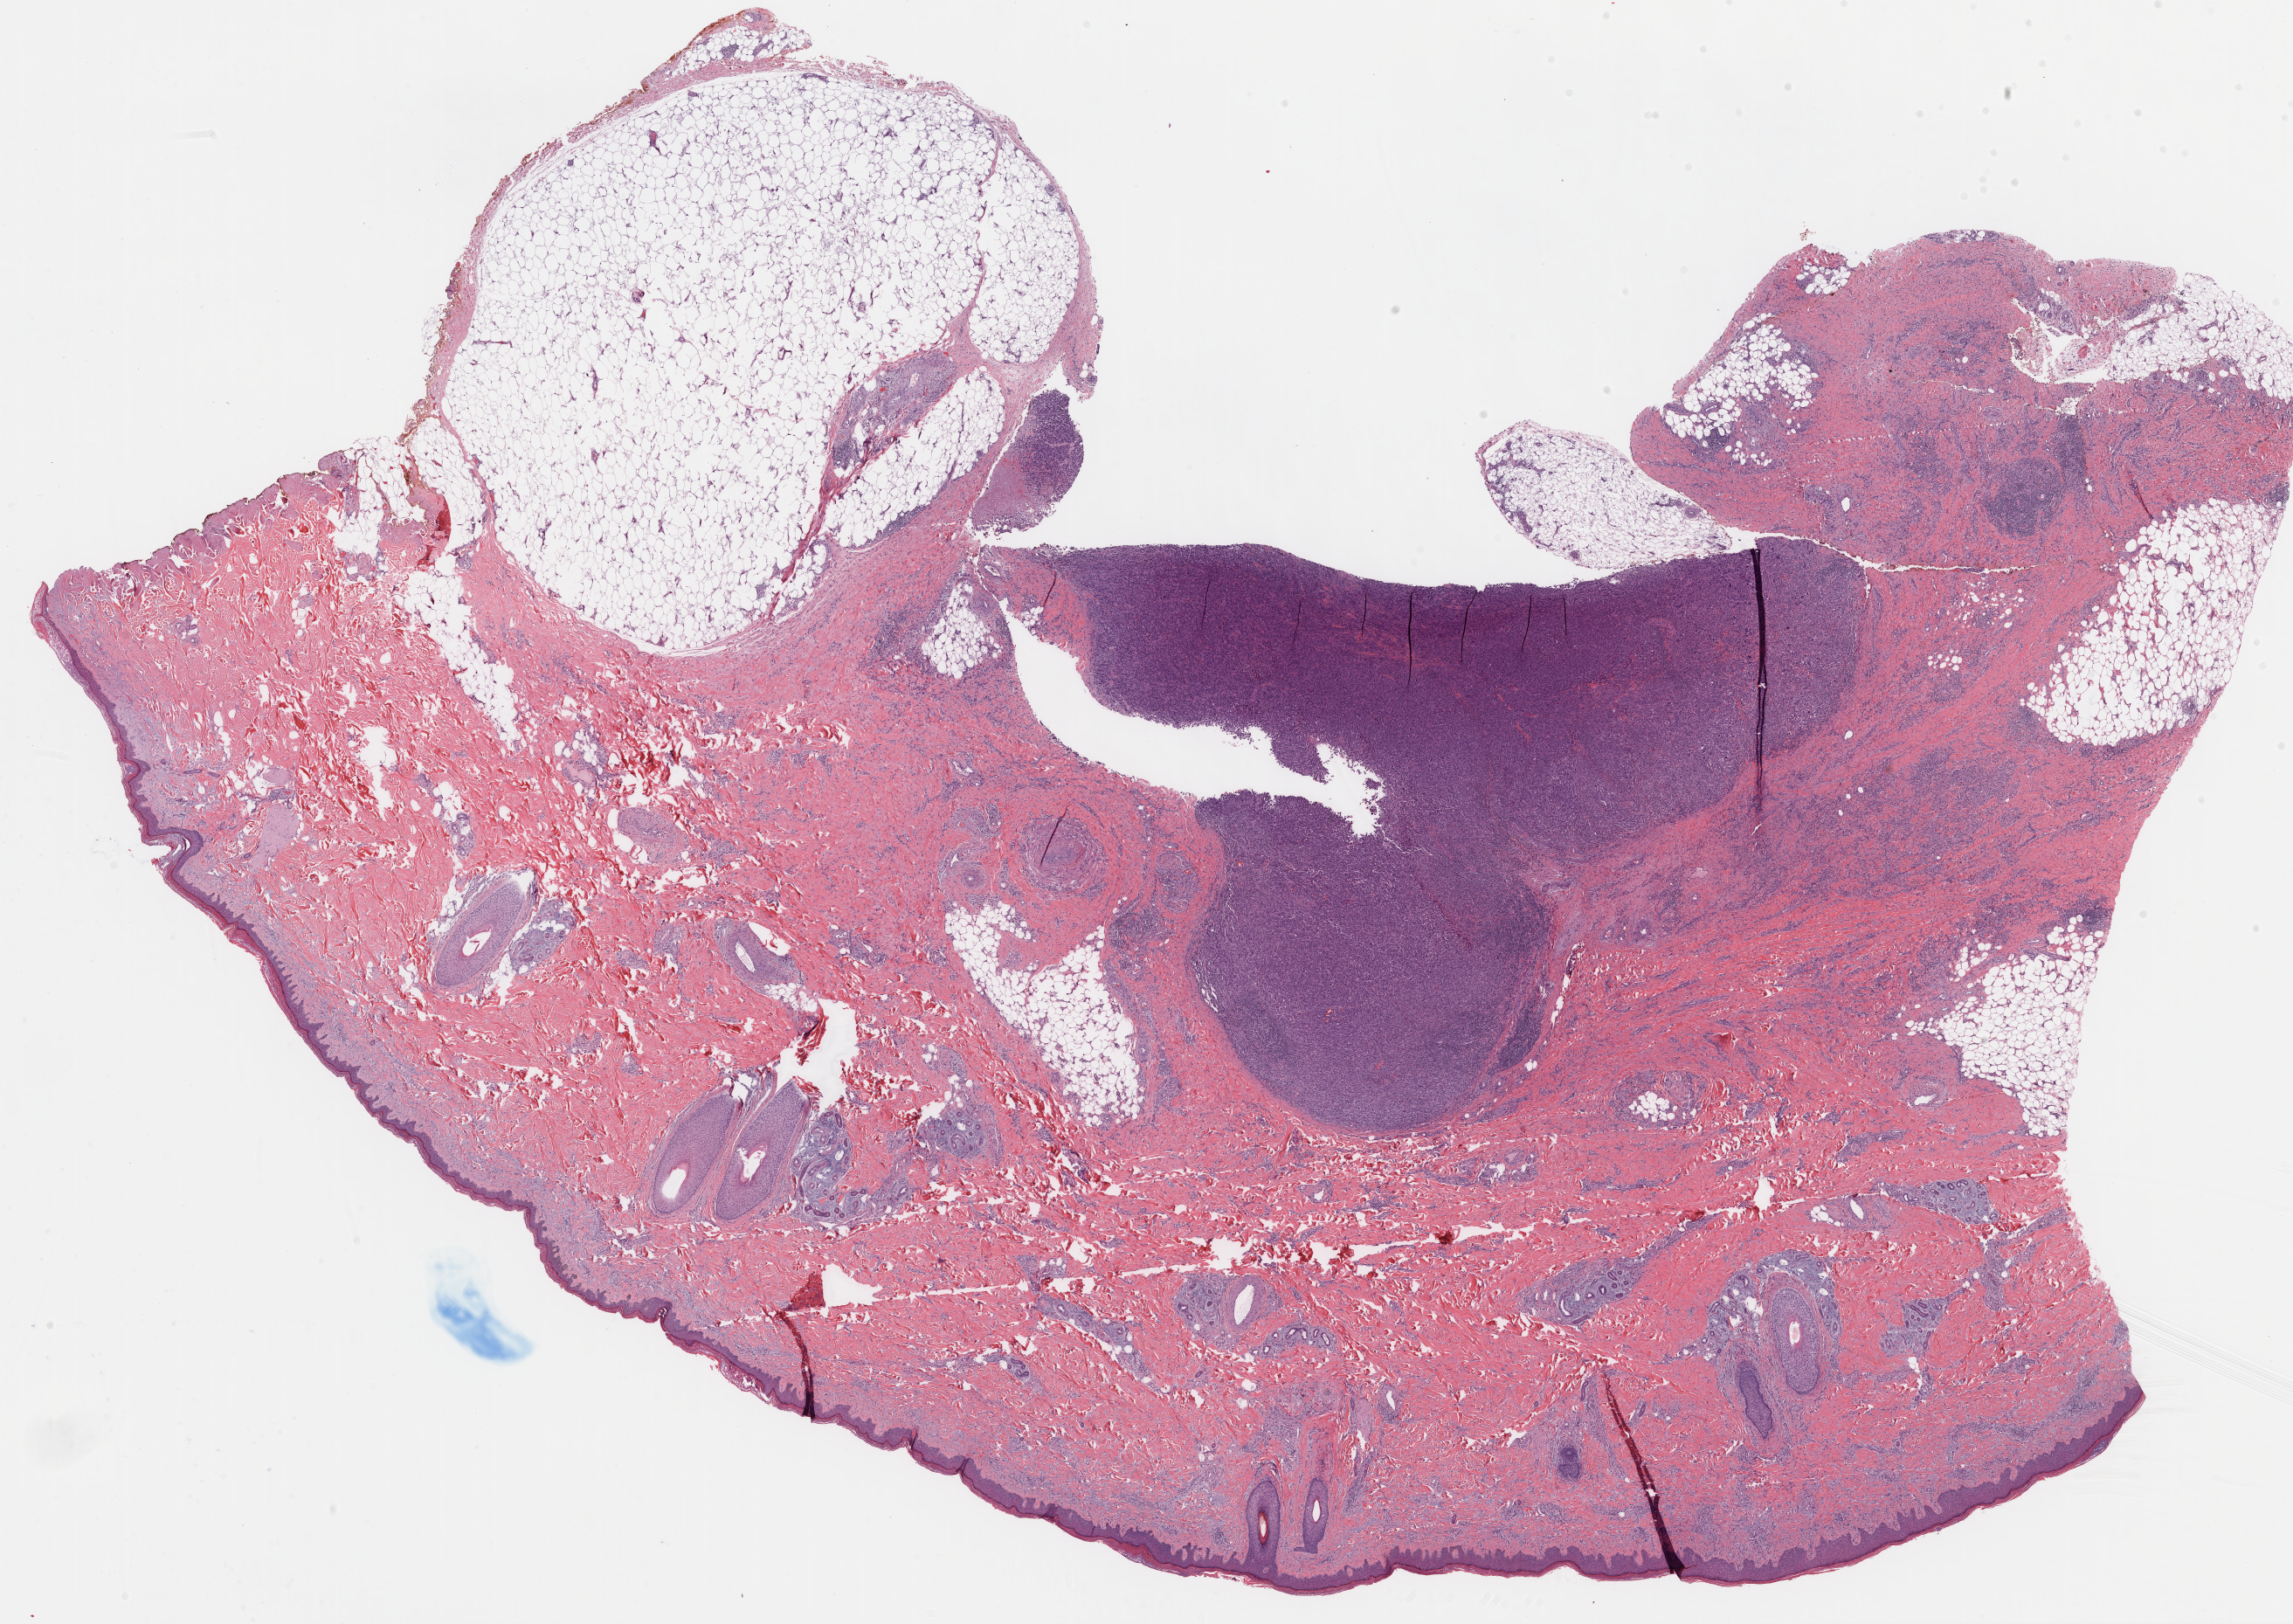
Digitized Hematoxylin and eosin (H&E) stained tissue section (whole slide) — a low-resolution overview of the entire scanned area, about 21.2 x 15.0 mm (acquisition: 20x scan). Formalin-fixed paraffin-embedded (FFPE) diagnostic section. Metastatic tumour sample, sampled site: lymph nodes of inguinal region or leg. Male patient; age at initial diagnosis 51 years.
This section: metastatic tumour tissue. Patient diagnosis: Malignant melanoma, NOS.